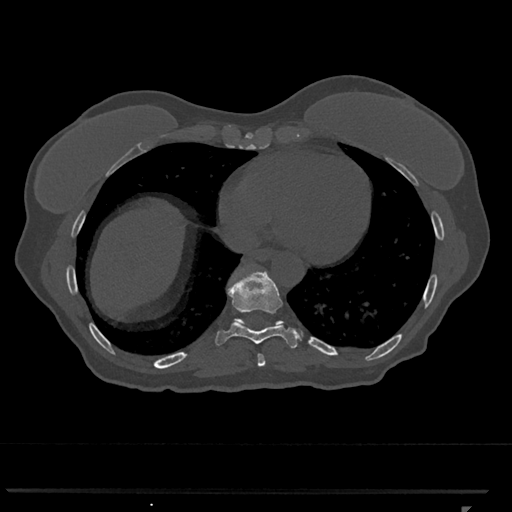
CT including the spine, one axial slice; slice 613 of 793 in the series (ordered by position); reconstruction kernel Br40s/3; 120 kVp; bone window (W 1800 / L 400 HU); 512 × 512 image matrix. Female patient, age 62 years. Case-level facts recorded for this patient, not image findings: primary cancer: renal.
Outlined on this slice (semi-automatically segmented with operator editing):
- T10 vertebra: bounding box <236,269,284,326> (left, top, right, bottom; pixels)
- T8 vertebra: <258,354,266,367>
- T9 vertebra: <215,271,301,349>